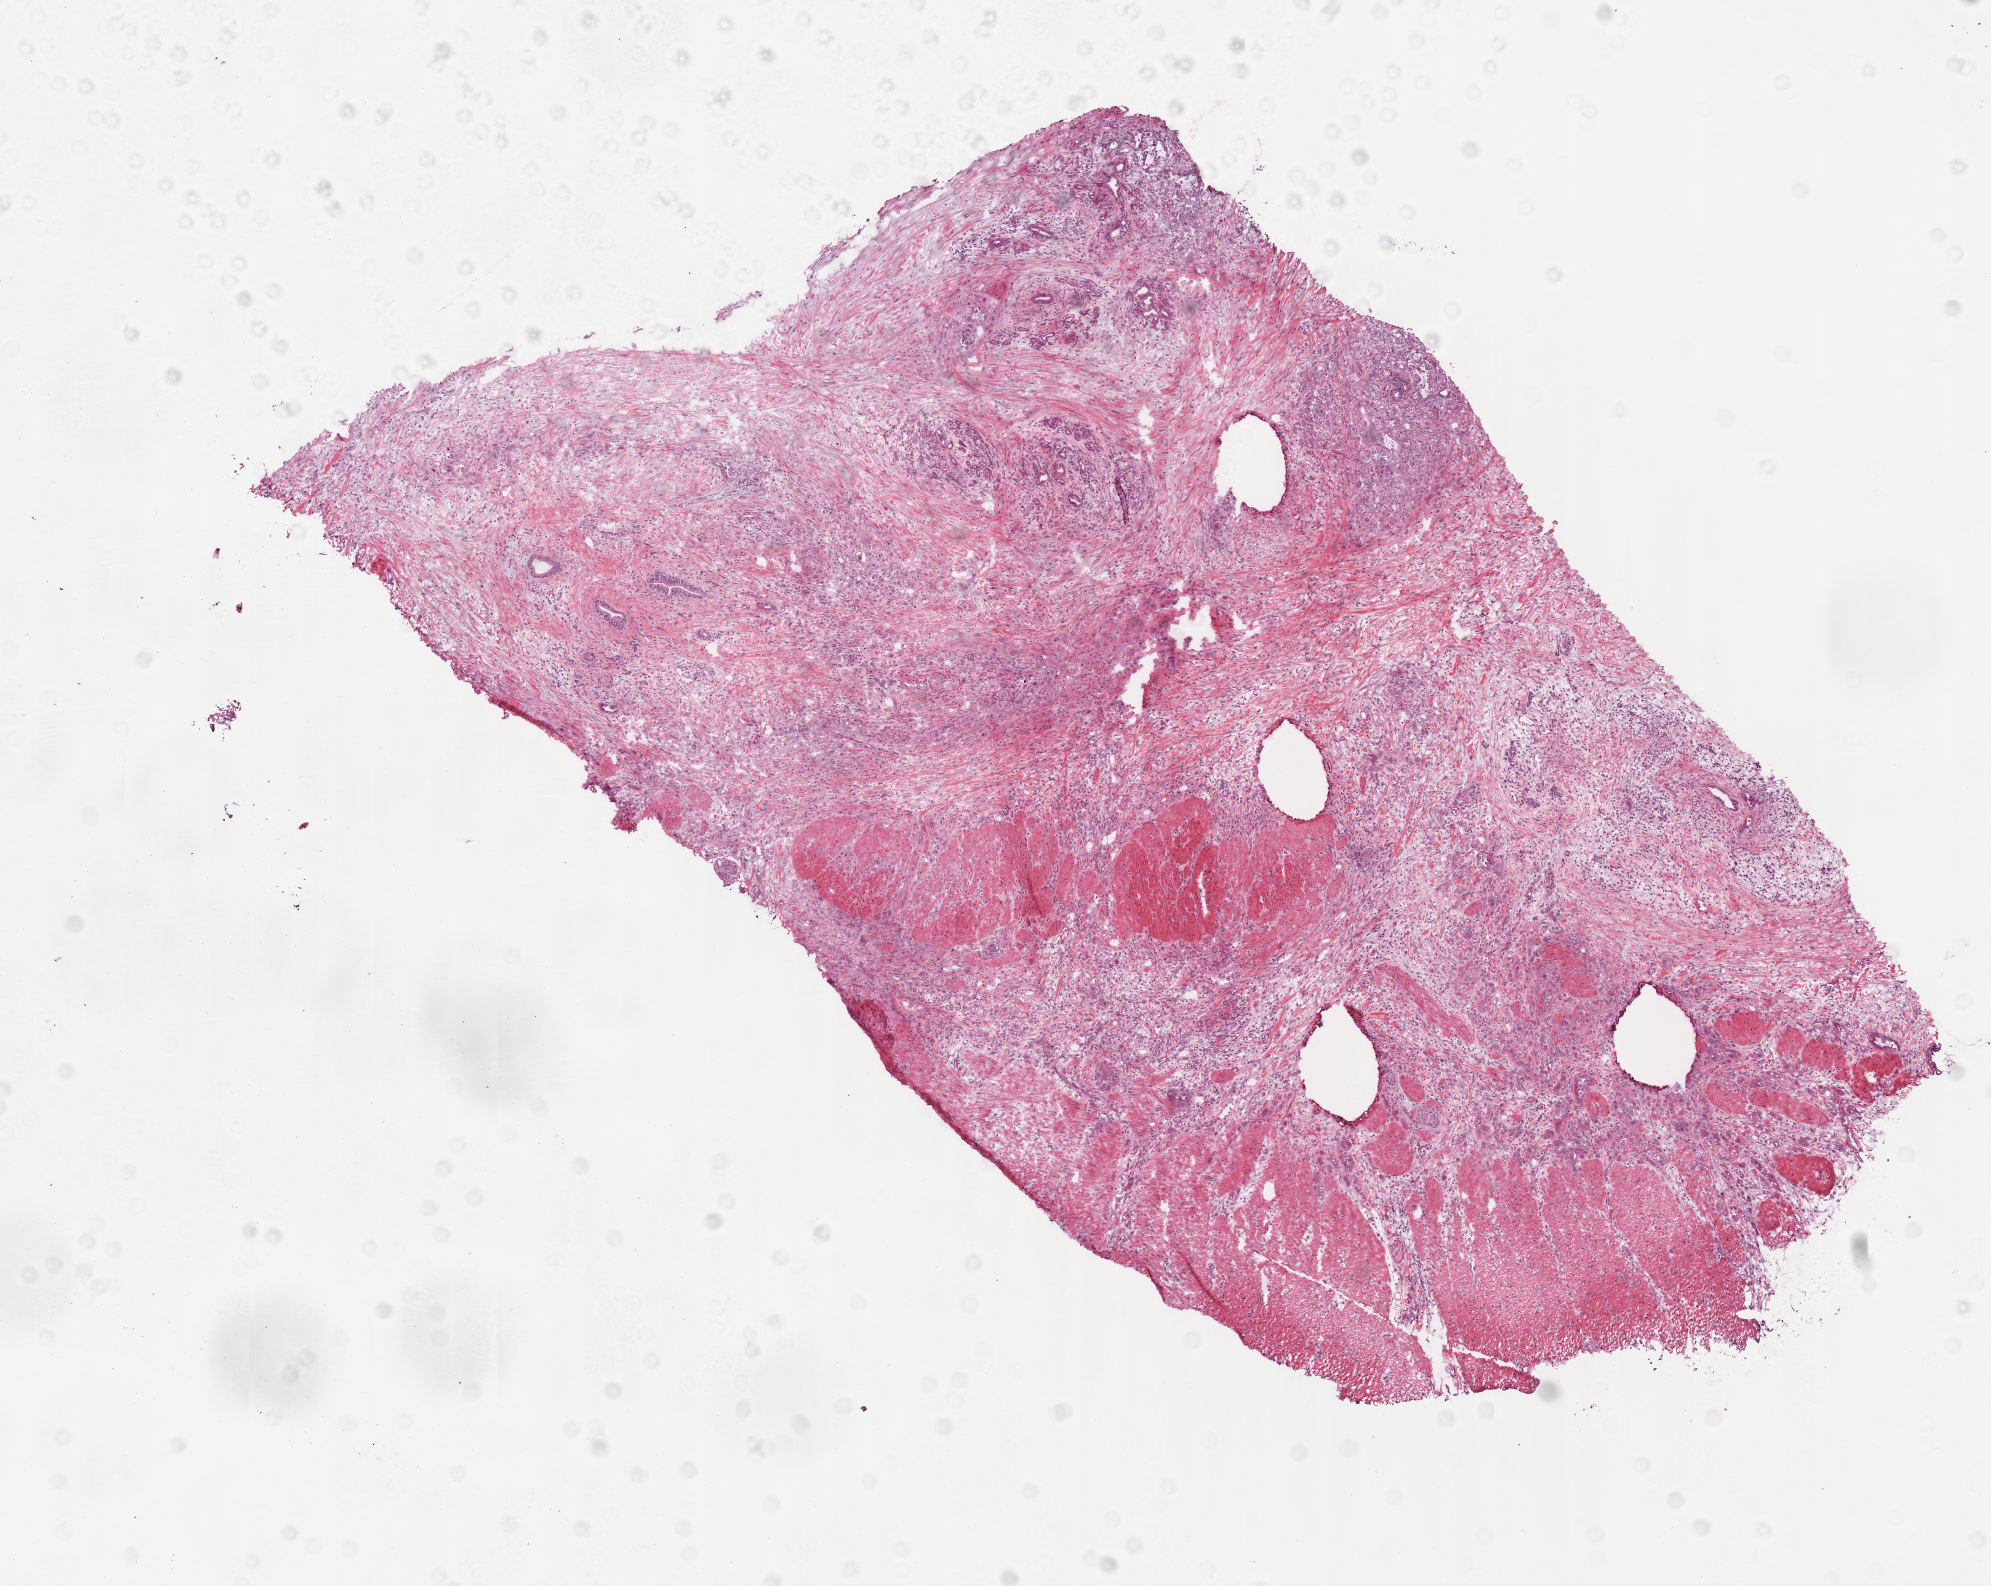
Whole-slide histology image, H&E — a low-resolution overview of the entire scanned area, about 8.1 x 6.4 mm; frozen section from the top of the tissue portion; sample: primary tumour, lung. Female patient; age at initial diagnosis 74 years. Slide review estimates, as recorded: tumour cells 95%, tumour nuclei 80%, normal cells 5%, stromal cells 0%, necrosis 0%.
• pathologic diagnosis: Bronchiolo-alveolar carcinoma, non-mucinous
• AJCC pathologic stage: IB (6th edition)